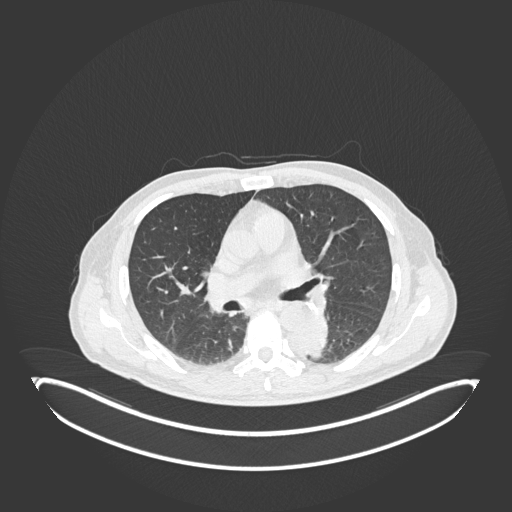
Chest CT, one axial slice; position 116 of 251 along the scan axis; reconstruction kernel B30f; lung window (W 1500 / L -600 HU); 512 × 512 image matrix. Male patient, age 72 years. From the clinical record (not read from this slice): clinical TNM (as recorded): T2b N0 M1.
Outlined on this slice (rectangle marked by the reading radiologist):
- lung tumour (recorded histology: adenocarcinoma): box from (x=286, y=315) to (x=330, y=363) px